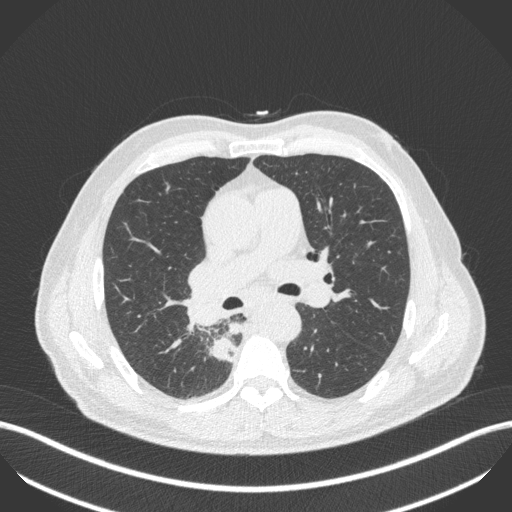
Chest CT, one axial slice; position 275 of 451 along the scan axis; 100 kVp; lung window (W 1500 / L -600 HU); 1 mm slice thickness; 512 × 512 image matrix, field of view 400 × 400 mm. Patient: male, 61 years. Case-level facts recorded for this patient, not image findings: clinical TNM (as recorded): T1 N0 M0; histopathological grade: G3.
Outlined on this slice (rectangle marked by the reading radiologist):
- lung tumour (recorded histology: small cell carcinoma): bounding box [x1, y1, x2, y2] px = [208, 333, 240, 371]